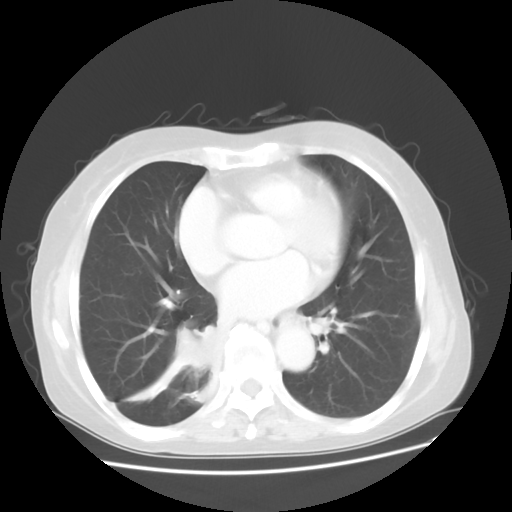
Chest CT, one axial slice. Slice 19 of 48 in the series (ordered by position). 120 kVp. Lung window (W 1500 / L -600 HU). 5 mm slice thickness. 512 × 512 image matrix, field of view 360 × 360 mm. Patient: female, 63 years. Case-level facts recorded for this patient, not image findings: clinical TNM (as recorded): T2 N3 M1b.
Outlined on this slice (bounding box drawn by a radiologist):
- lung tumour (recorded histology: small cell carcinoma): box from (x=171, y=318) to (x=221, y=377) px